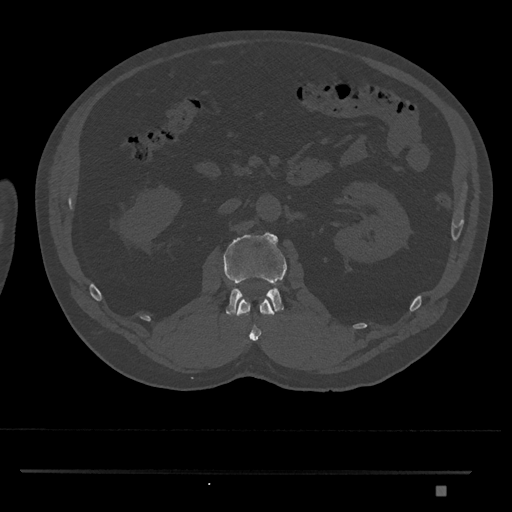
CT including the spine, one axial slice; position 781 of 1134 along the scan axis; 120 kVp; bone window (W 1800 / L 400 HU); 512 × 512 image matrix, field of view 429 × 429 mm. Patient: male, 65 years. Case-level facts recorded for this patient, not image findings: primary cancer: prostate.
Annotated regions visible in this slice (semi-automatic segmentation, software-assisted and operator-edited):
- L1 vertebra: bounding box [x1, y1, x2, y2] px = [236, 297, 275, 341]
- L2 vertebra: [223, 232, 287, 316]